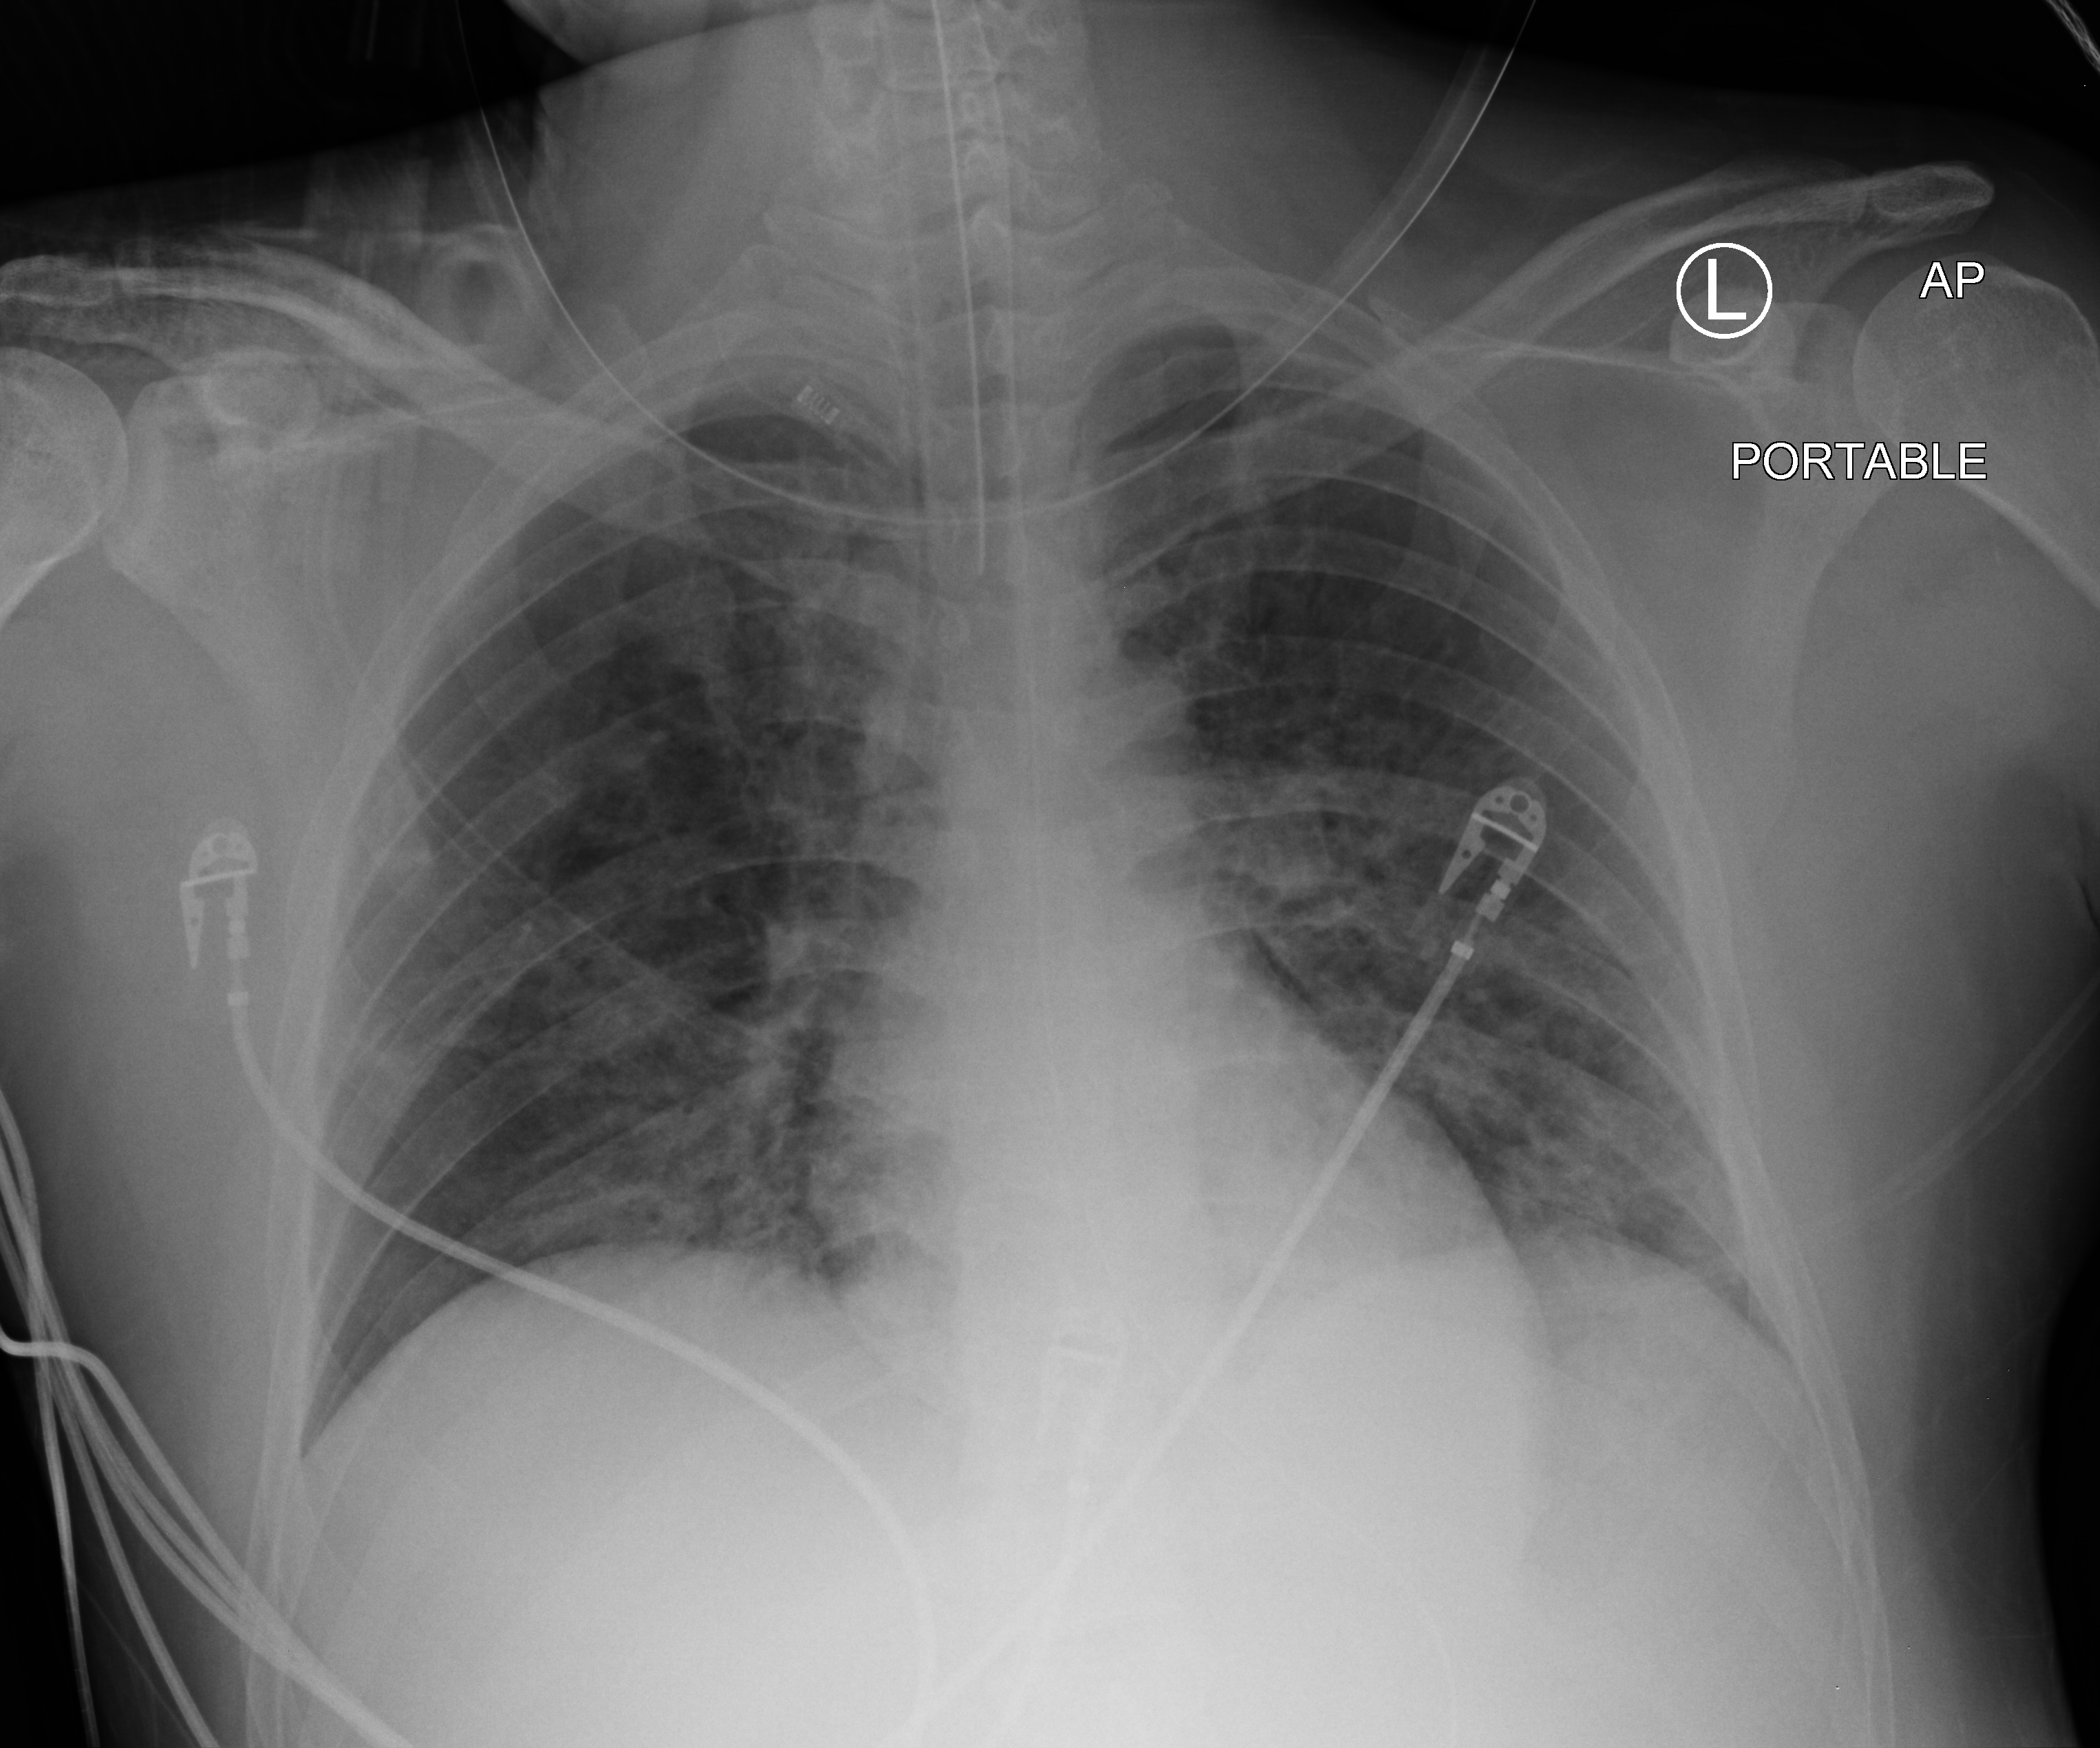
Portable chest radiograph, anteroposterior (AP) projection. Patient hospitalised with COVID-19, aged 18–59 years.
From the hospital-stay record, not from the radiograph (when in the stay this image was taken is not recorded): admitted to intensive care during this hospital stay: yes; mechanically ventilated during this hospital stay: yes; diabetes (admission record): no.